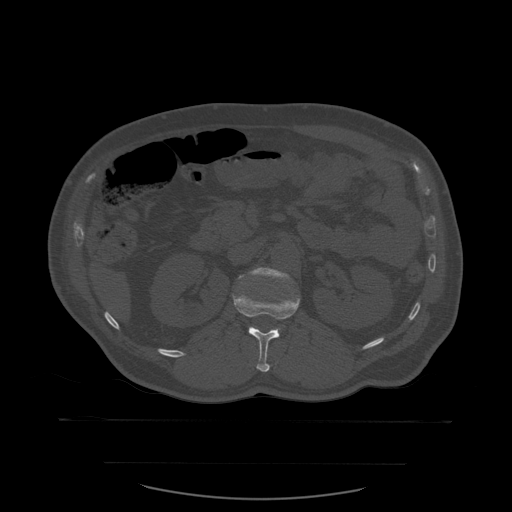
CT including the spine, one axial slice. Position 240 of 590 along the scan axis. Bone window (W 1800 / L 400 HU). 1.25 mm slice thickness. 512 × 512 image matrix. Patient age 71 years. From the clinical record (not read from this slice): primary cancer: lung.
Outlined on this slice (semi-automatic segmentation, software-assisted and operator-edited):
- L1 vertebra: bounding box (x1, y1, x2, y2) in pixels: (233, 274, 300, 372)
- L2 vertebra: (239, 268, 287, 332)